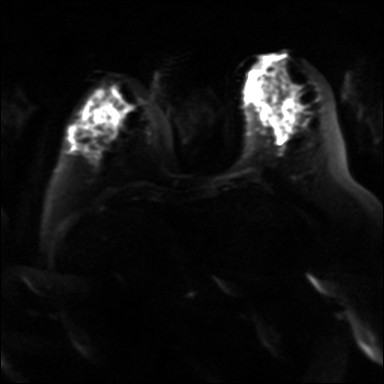
Breast MRI, one axial slice; slice 11 of 36 in the series (ordered by position); diffusion-weighted series; image 2 of 4 stored at this slice position (different b-values; order by instance number); 3 T; 4 mm slice thickness; 384 × 384 image matrix, field of view 320 × 320 mm. Female patient.
Structures marked on this image (outlined manually by an expert reader):
- tumour on diffusion-weighted imaging: box from (x=286, y=135) to (x=292, y=141) px